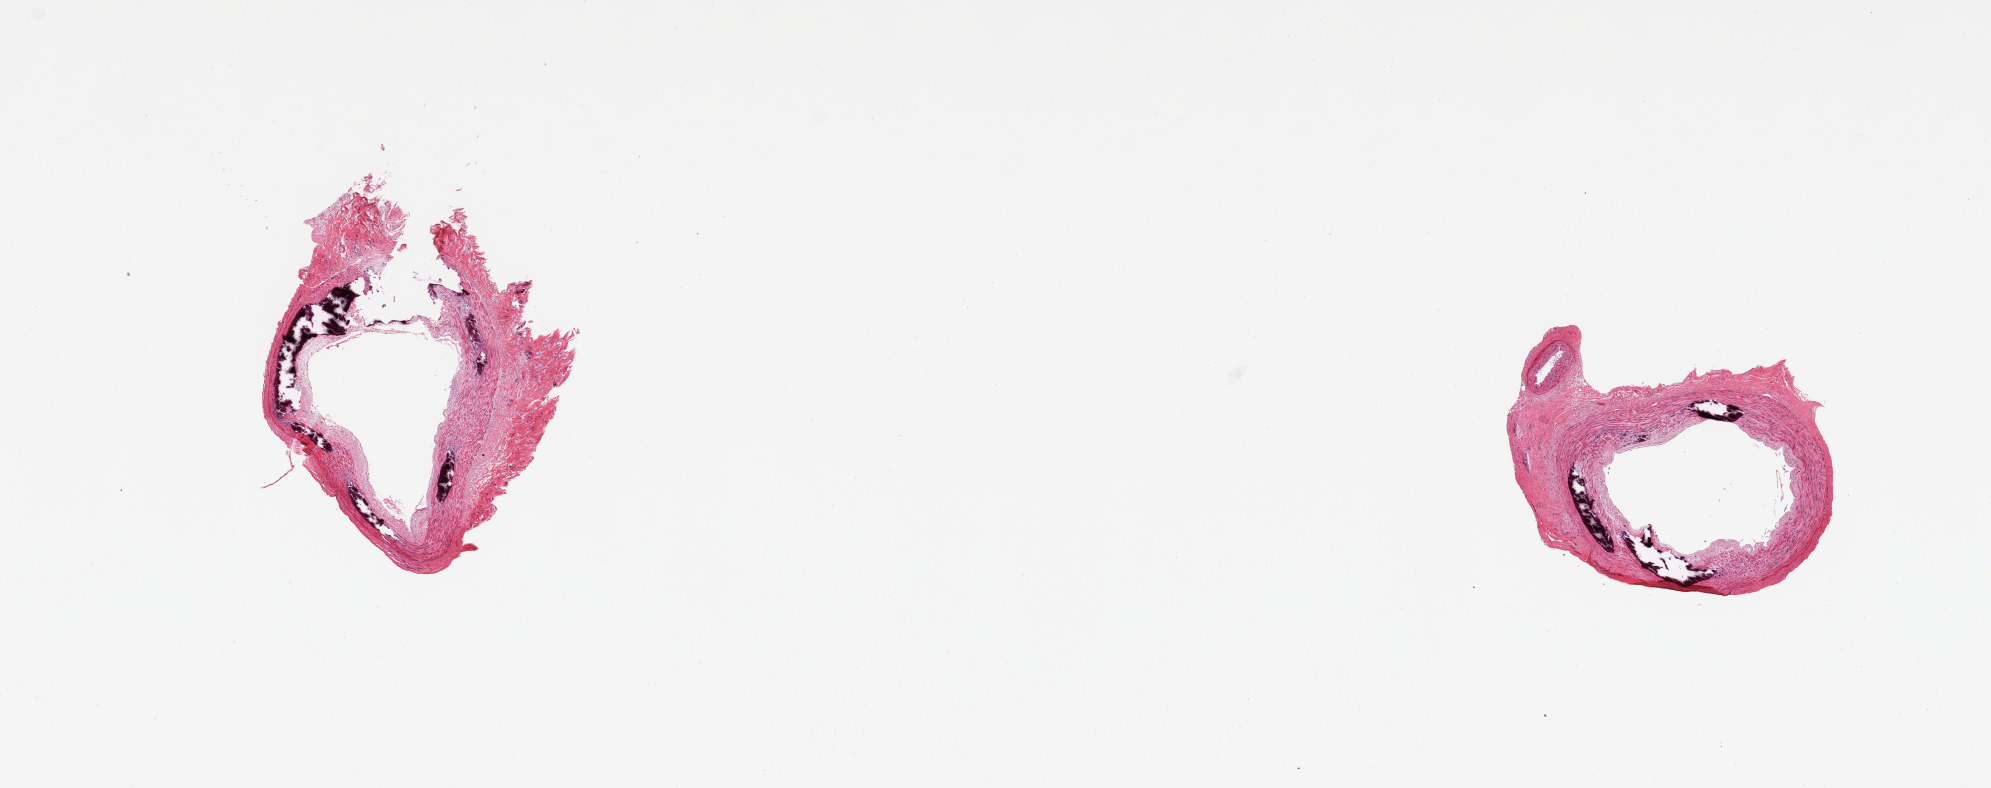
Whole-slide image, hematoxylin and eosin (H&E) stain, whole scanned area (about 15.8 x 6.2 mm) shown as a low-resolution overview; PAXgene-fixed, paraffin-embedded tissue; sampled site (target tissue): tibial artery; tissue donor sample. Donor sex: male.
• pathologist's review note for this sample: 2 pieces, trace atherosis; prominent Monckeberg sclerosis